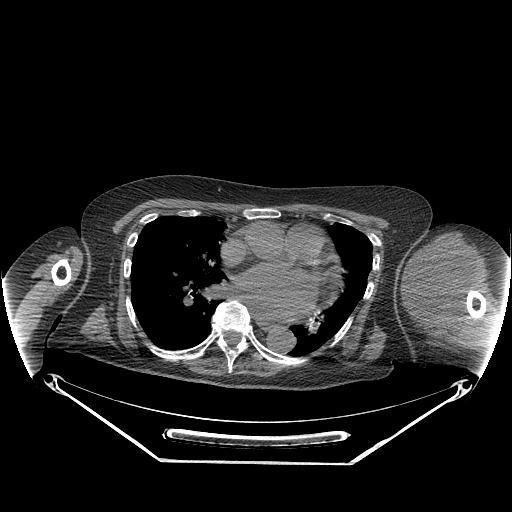
CT of an extremity soft-tissue mass (from a PET/CT study), one axial slice; position 171 of 267 along the scan axis; 140 kVp; soft-tissue window (W 400 / L 40 HU); 3.75 mm slice thickness; 512 × 512 image matrix, field of view 500 × 500 mm. Female patient. From the clinical record (not read from this slice): histological type: pleiomorphic leiomyosarcoma; grade: high; site of the primary tumour: left biceps.
Structures marked on this image (expert contour drawn on MRI and transferred to this co-registered scan by the dataset authors):
- gross tumour volume including surrounding oedema: bounding box <402,233,481,330> (left, top, right, bottom; pixels)
- gross tumour volume (mass): <404,233,474,323>